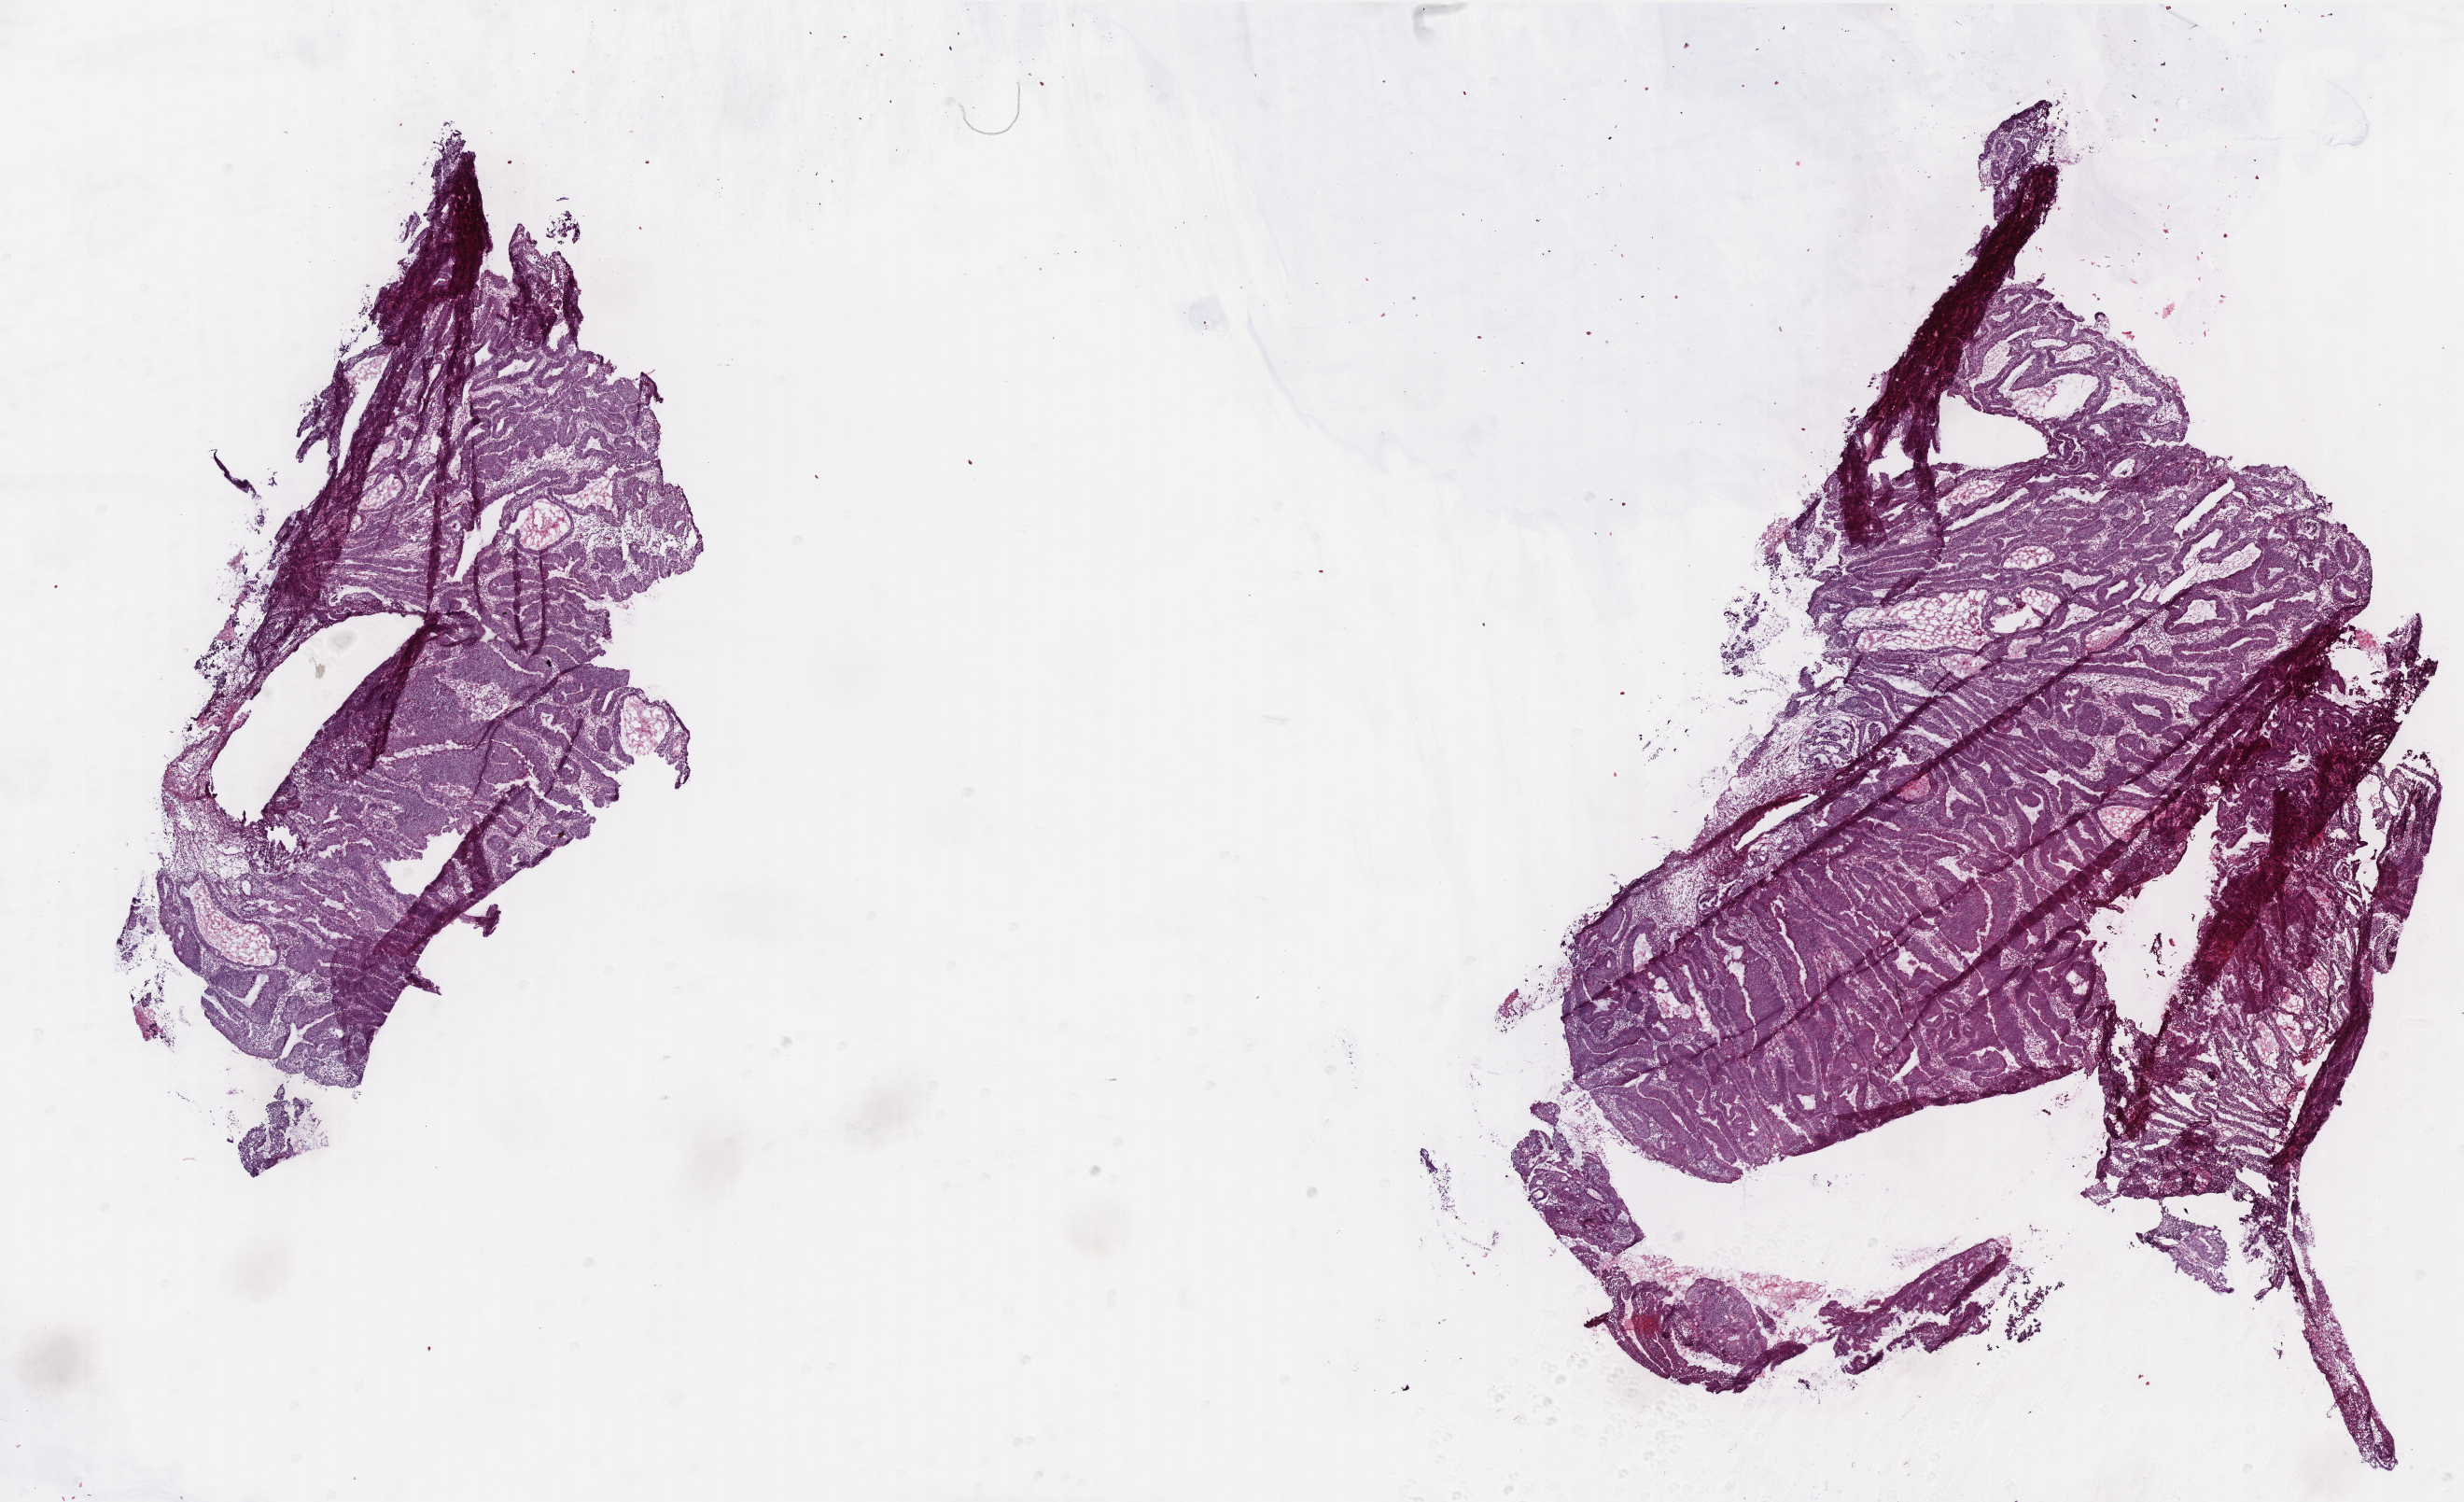
Digitized H&E tissue section (whole slide), low-resolution overview of the scanned area, about 21.2 x 12.9 mm. Frozen section. Sample: primary tumour, colon. Patient: male, age at initial diagnosis 59 years. Composition of this section per pathologist review: tumour cells 95%, tumour nuclei 90%, normal cells 0%, stromal cells 4%, necrosis 1%. Infiltration values recorded for this section: lymphocyte infiltration 4%, monocyte infiltration 1%, neutrophil infiltration 1%.
- histologic diagnosis: Adenocarcinoma, NOS (cecum)
- lymph nodes positive (case pathology): 0 of 15 examined
- TNM: T2 N0 M0
- AJCC pathologic stage: I